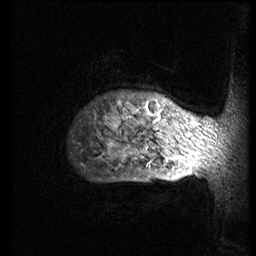
Breast MRI (dynamic contrast-enhanced), one sagittal slice. Slice 67 of 74 in the series (ordered by position). 3 images stored at this slice position (order not interpretable as contrast timing). 1.5 T. TE 4.2 ms, TR 8.9 ms. 2.5 mm slice thickness. 256 × 256 image matrix, field of view 200 × 200 mm. Female patient, age 57 years. From the clinical record (not read from this slice): setting: breast cancer imaged before/during neoadjuvant chemotherapy; receptor status: HER2-positive.
Outlined on this slice (semi-automatic segmentation, software-assisted and operator-edited):
- analysis volume of interest (the breast-tissue region the enhancement analysis was run in; not a lesion): bounding box (x1, y1, x2, y2) in pixels: (70, 78, 248, 173)
- tumour enhancement mask (voxels above the 140 % enhancement threshold inside the analysis volume of interest): (150, 113, 218, 172)